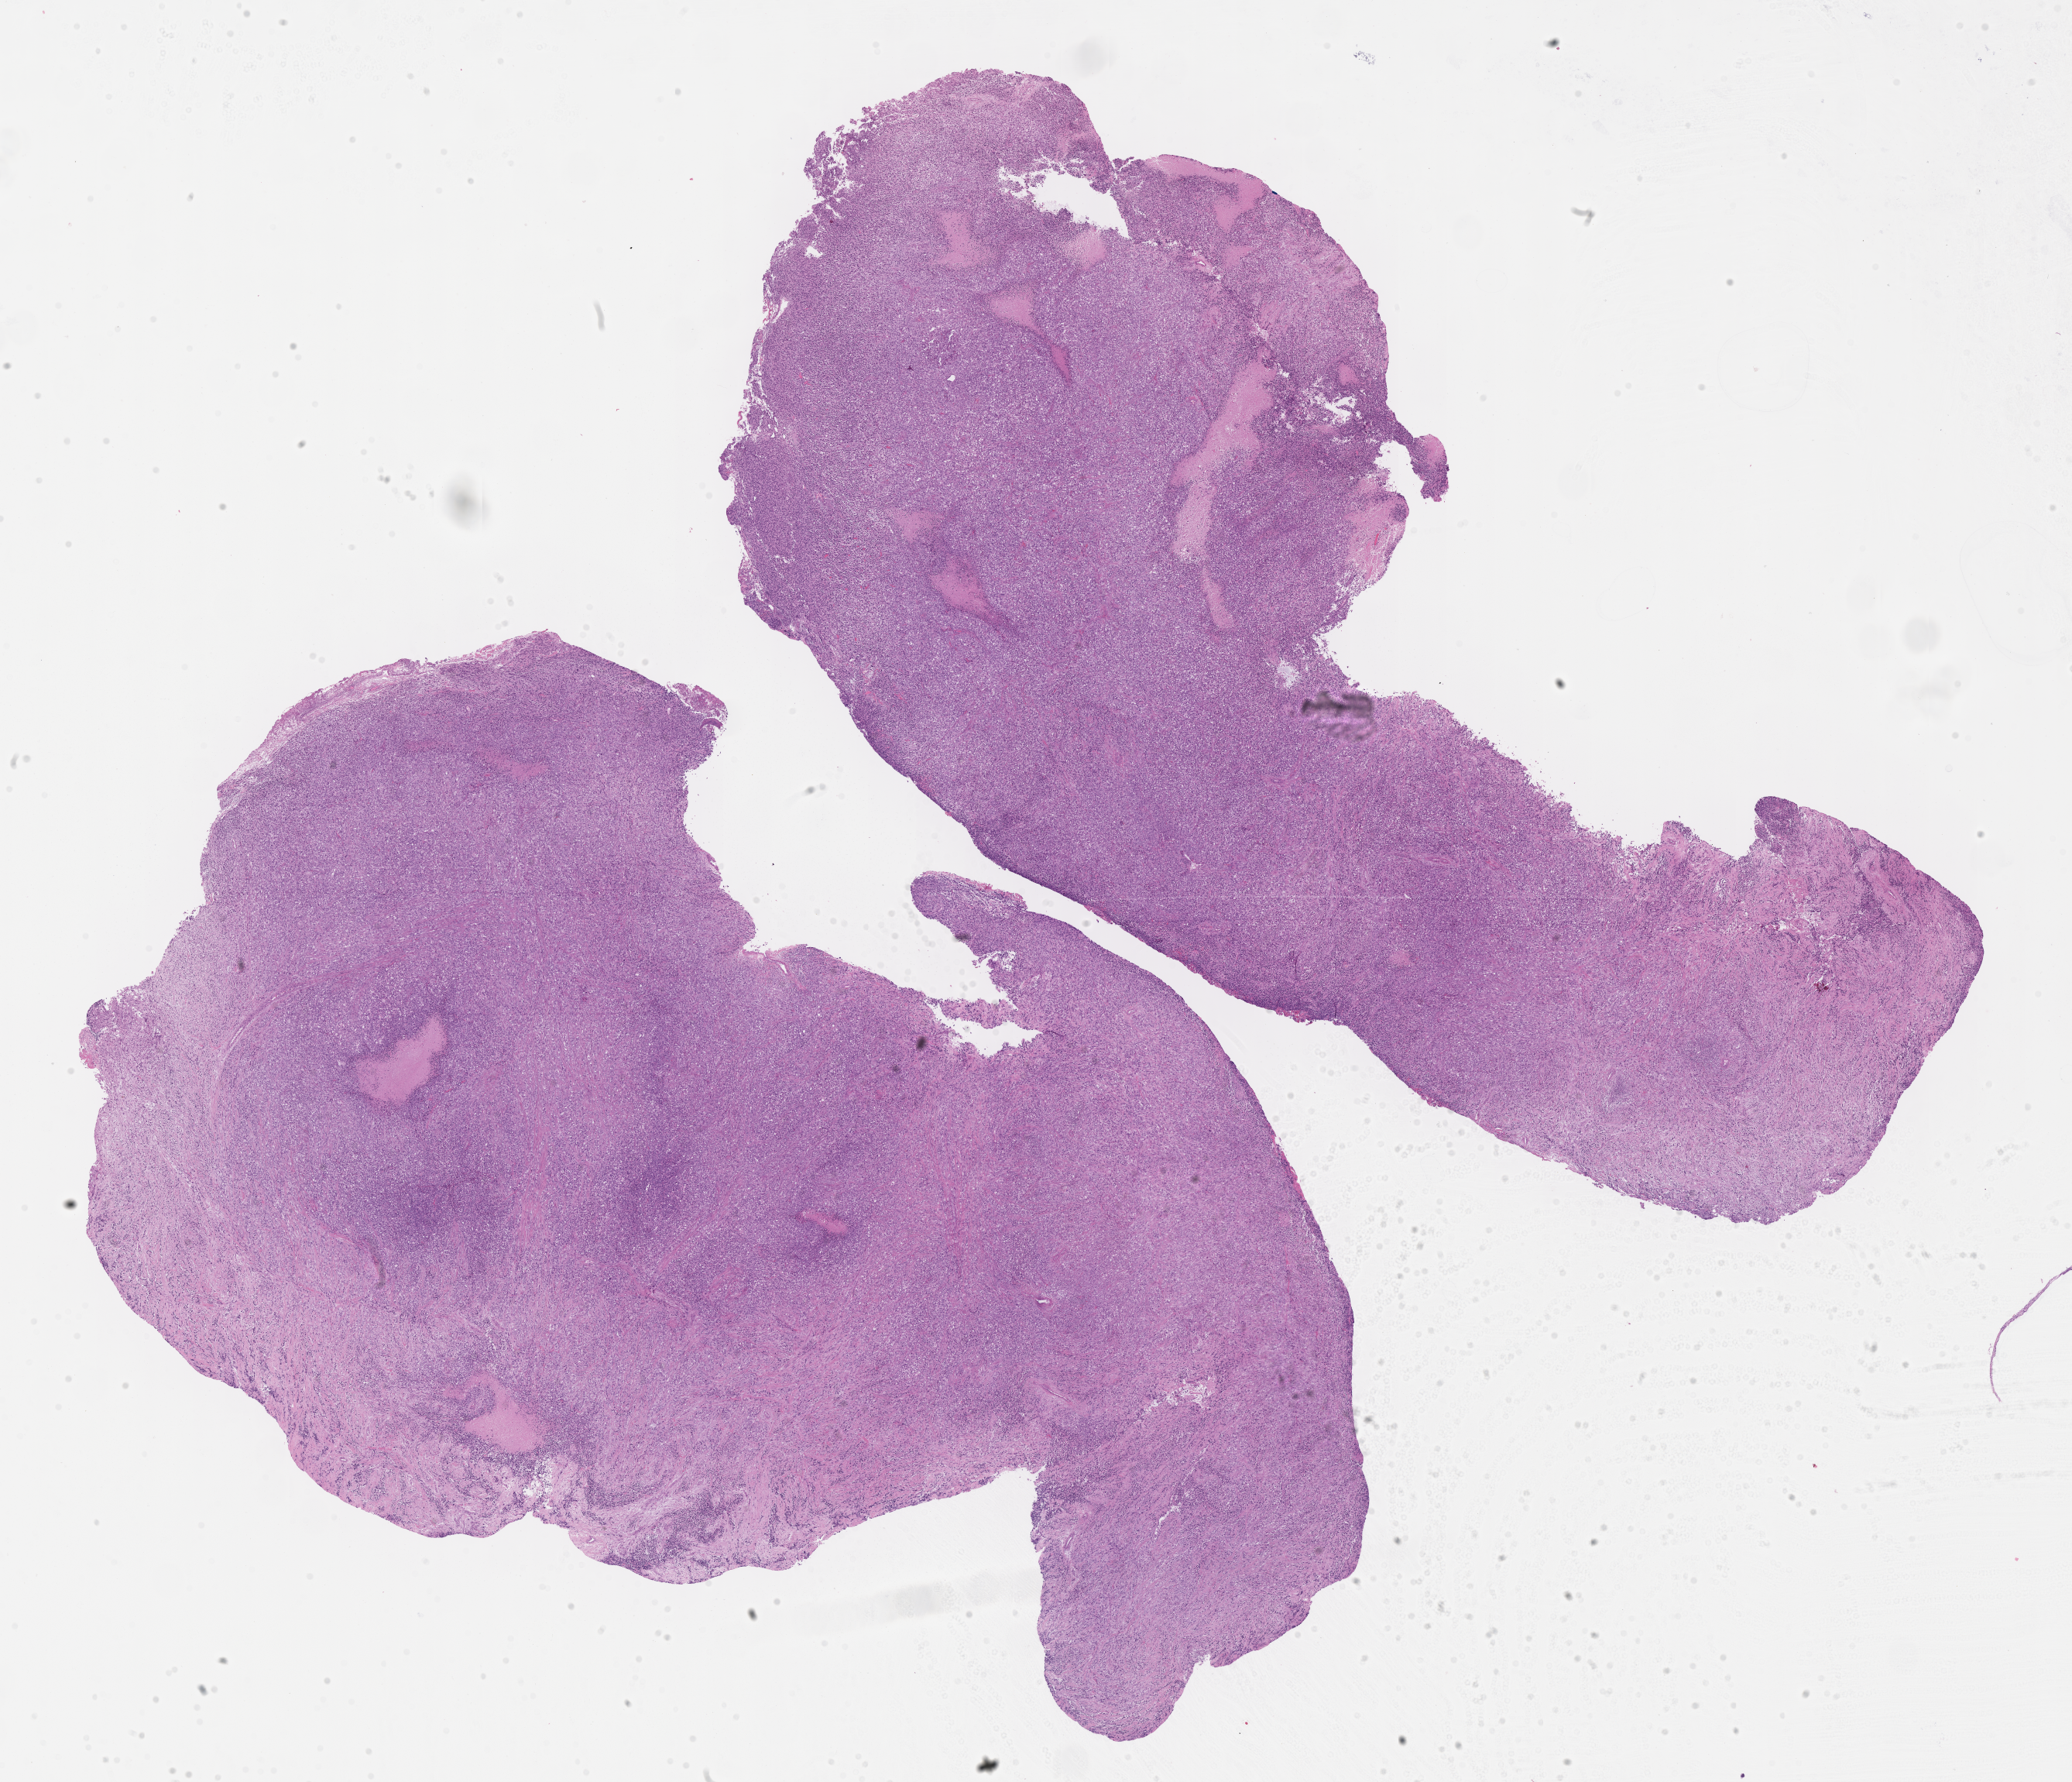
Digitized H&E-stained section of tumor tissue — a low-resolution overview of the entire scanned area, about 21.6 x 18.6 mm. Formalin-fixed, paraffin-embedded (FFPE) tissue. Site: soft tissue, scalp. Patient: male, age 12.7 years at diagnosis.
Primary site (case record): other head & neck. Stage (as recorded): 4. Metastatic status at presentation (as recorded): metastatic (confirmed). Diagnosis: rhabdomyosarcoma; histological classification: embryonal rhabdomyosarcoma.